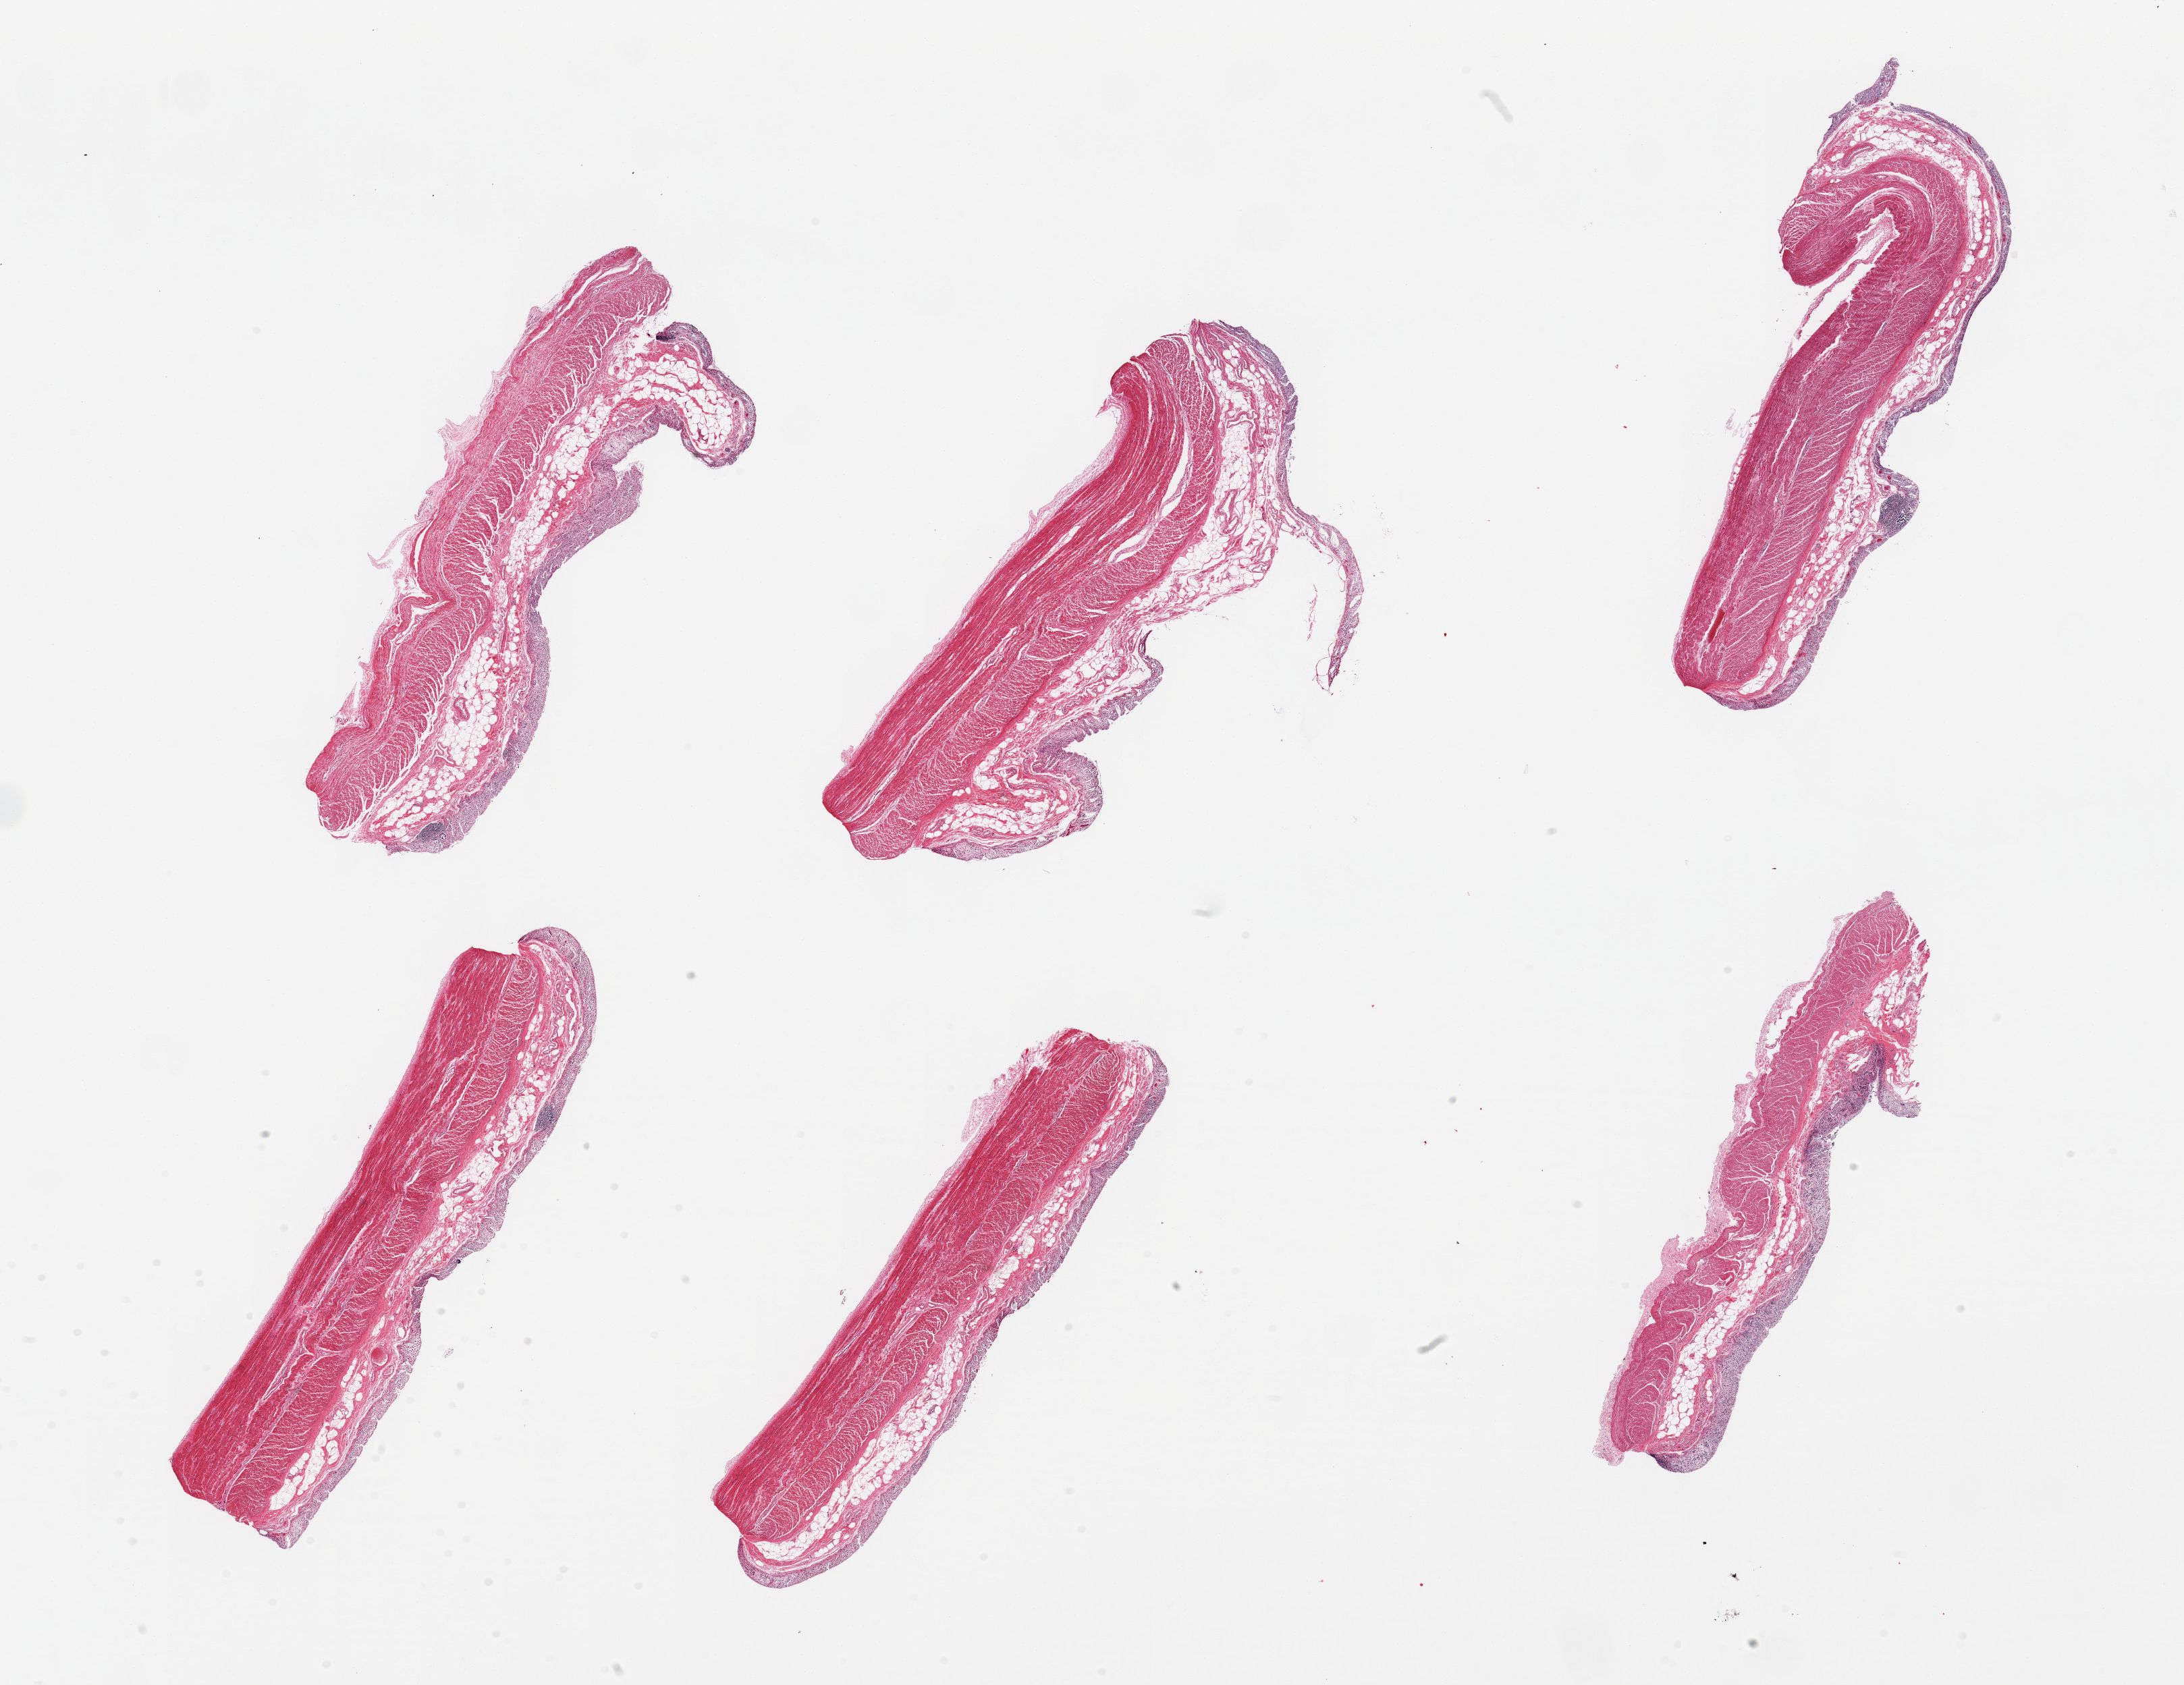
Digitized H&E-stained section, shown as a low-resolution overview of the whole scanned area (about 25.6 x 19.7 mm), PAXgene-fixed, paraffin-embedded tissue, target tissue: transverse colon, tissue donor sample. Donor sex: male.
- reviewer comment on this tissue sample: 6 pieces, mucosa up to ~-.3mm, advanced autolysis, glandular elements sloughed